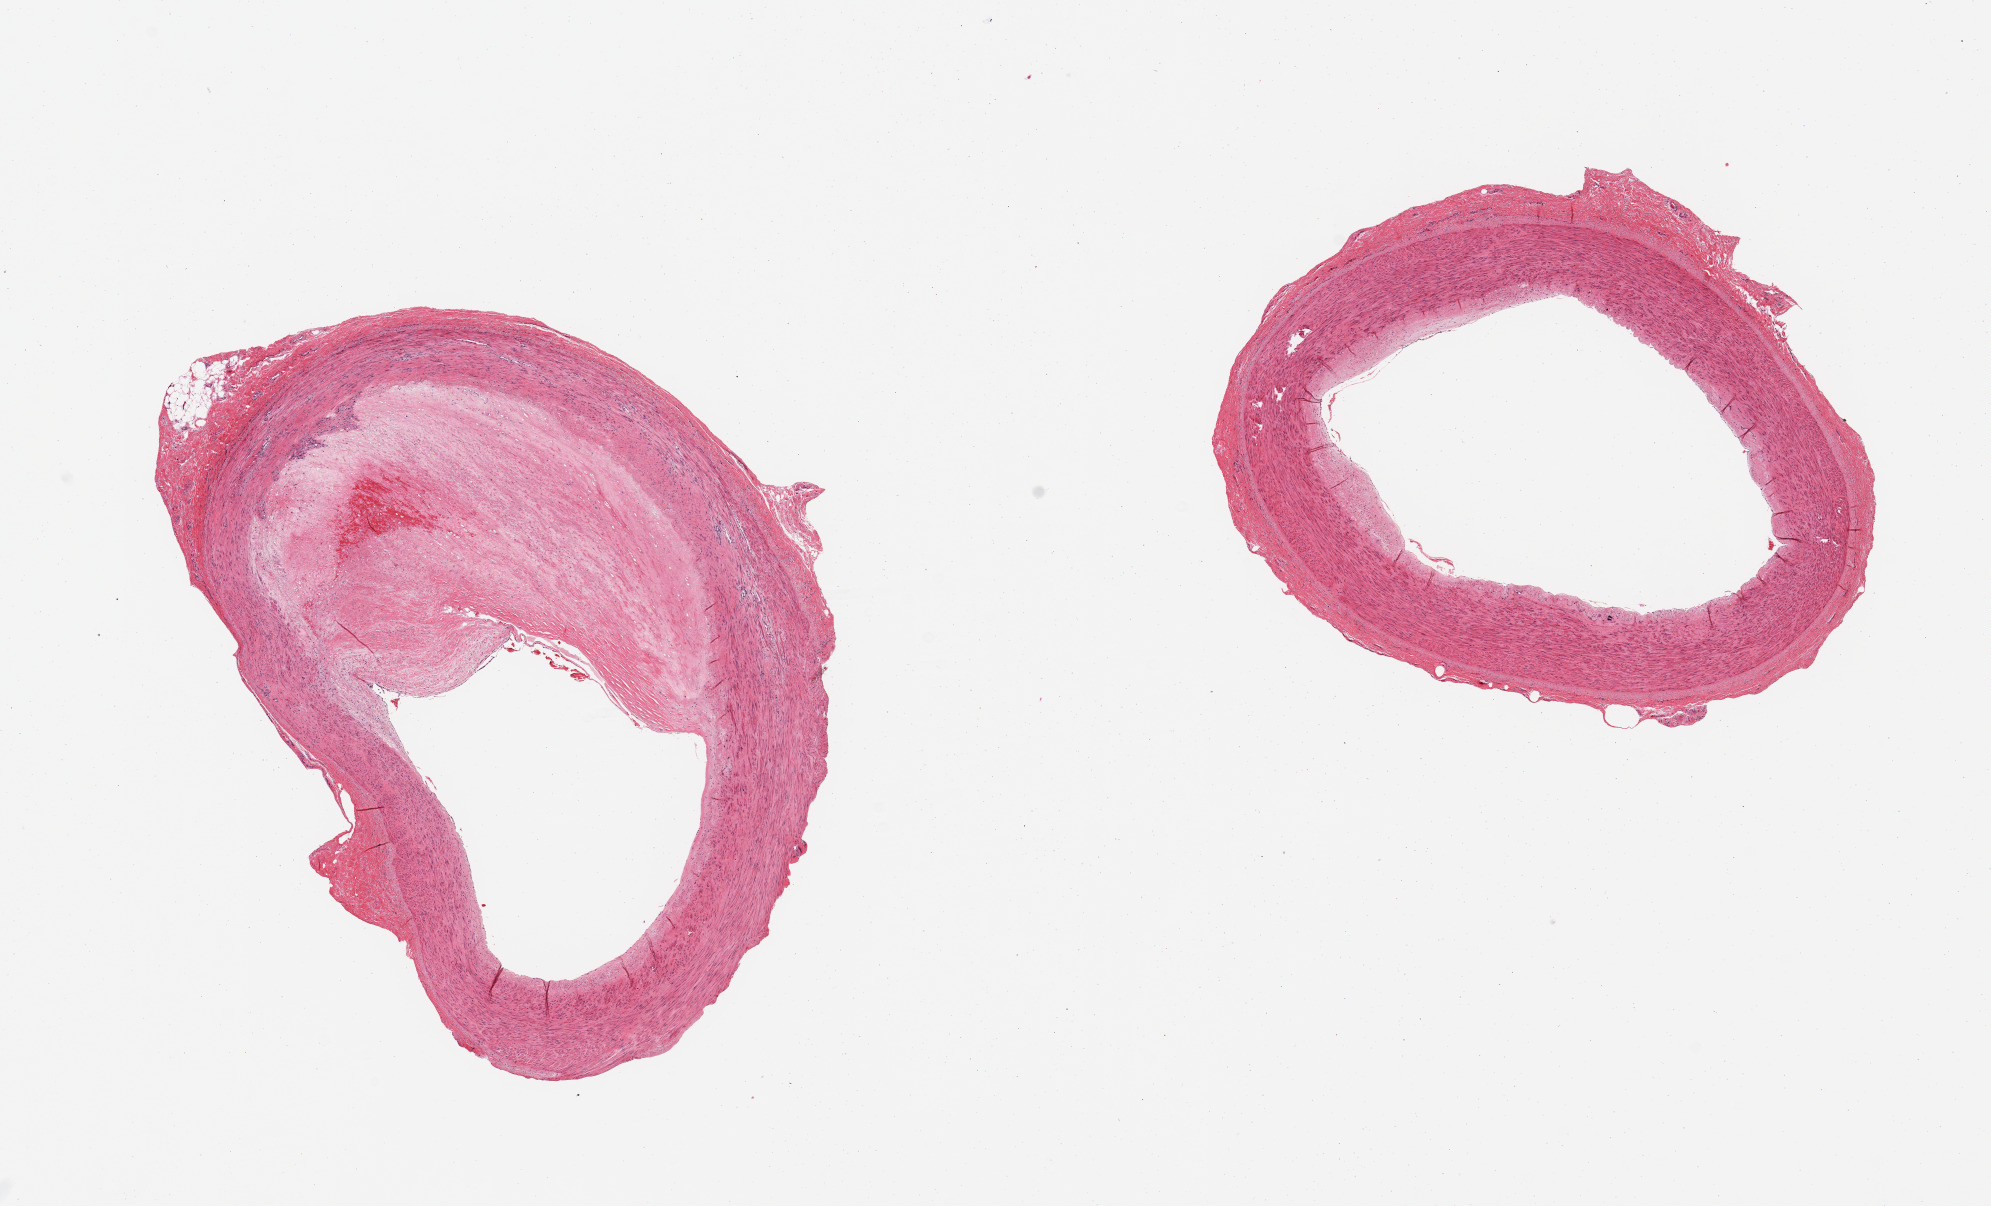
Digitized haematoxylin and eosin-stained section, brightfield — low-resolution overview of the scanned area, about 15.8 x 9.5 mm (from a 20x scan), PAXgene-fixed, paraffin-embedded tissue, sampled site (target tissue): tibial artery, donor tissue sample. Donor: male.
Reviewer comment on this tissue sample: 2 pieces, ~50% occlusive atherosis; good clean specimens.